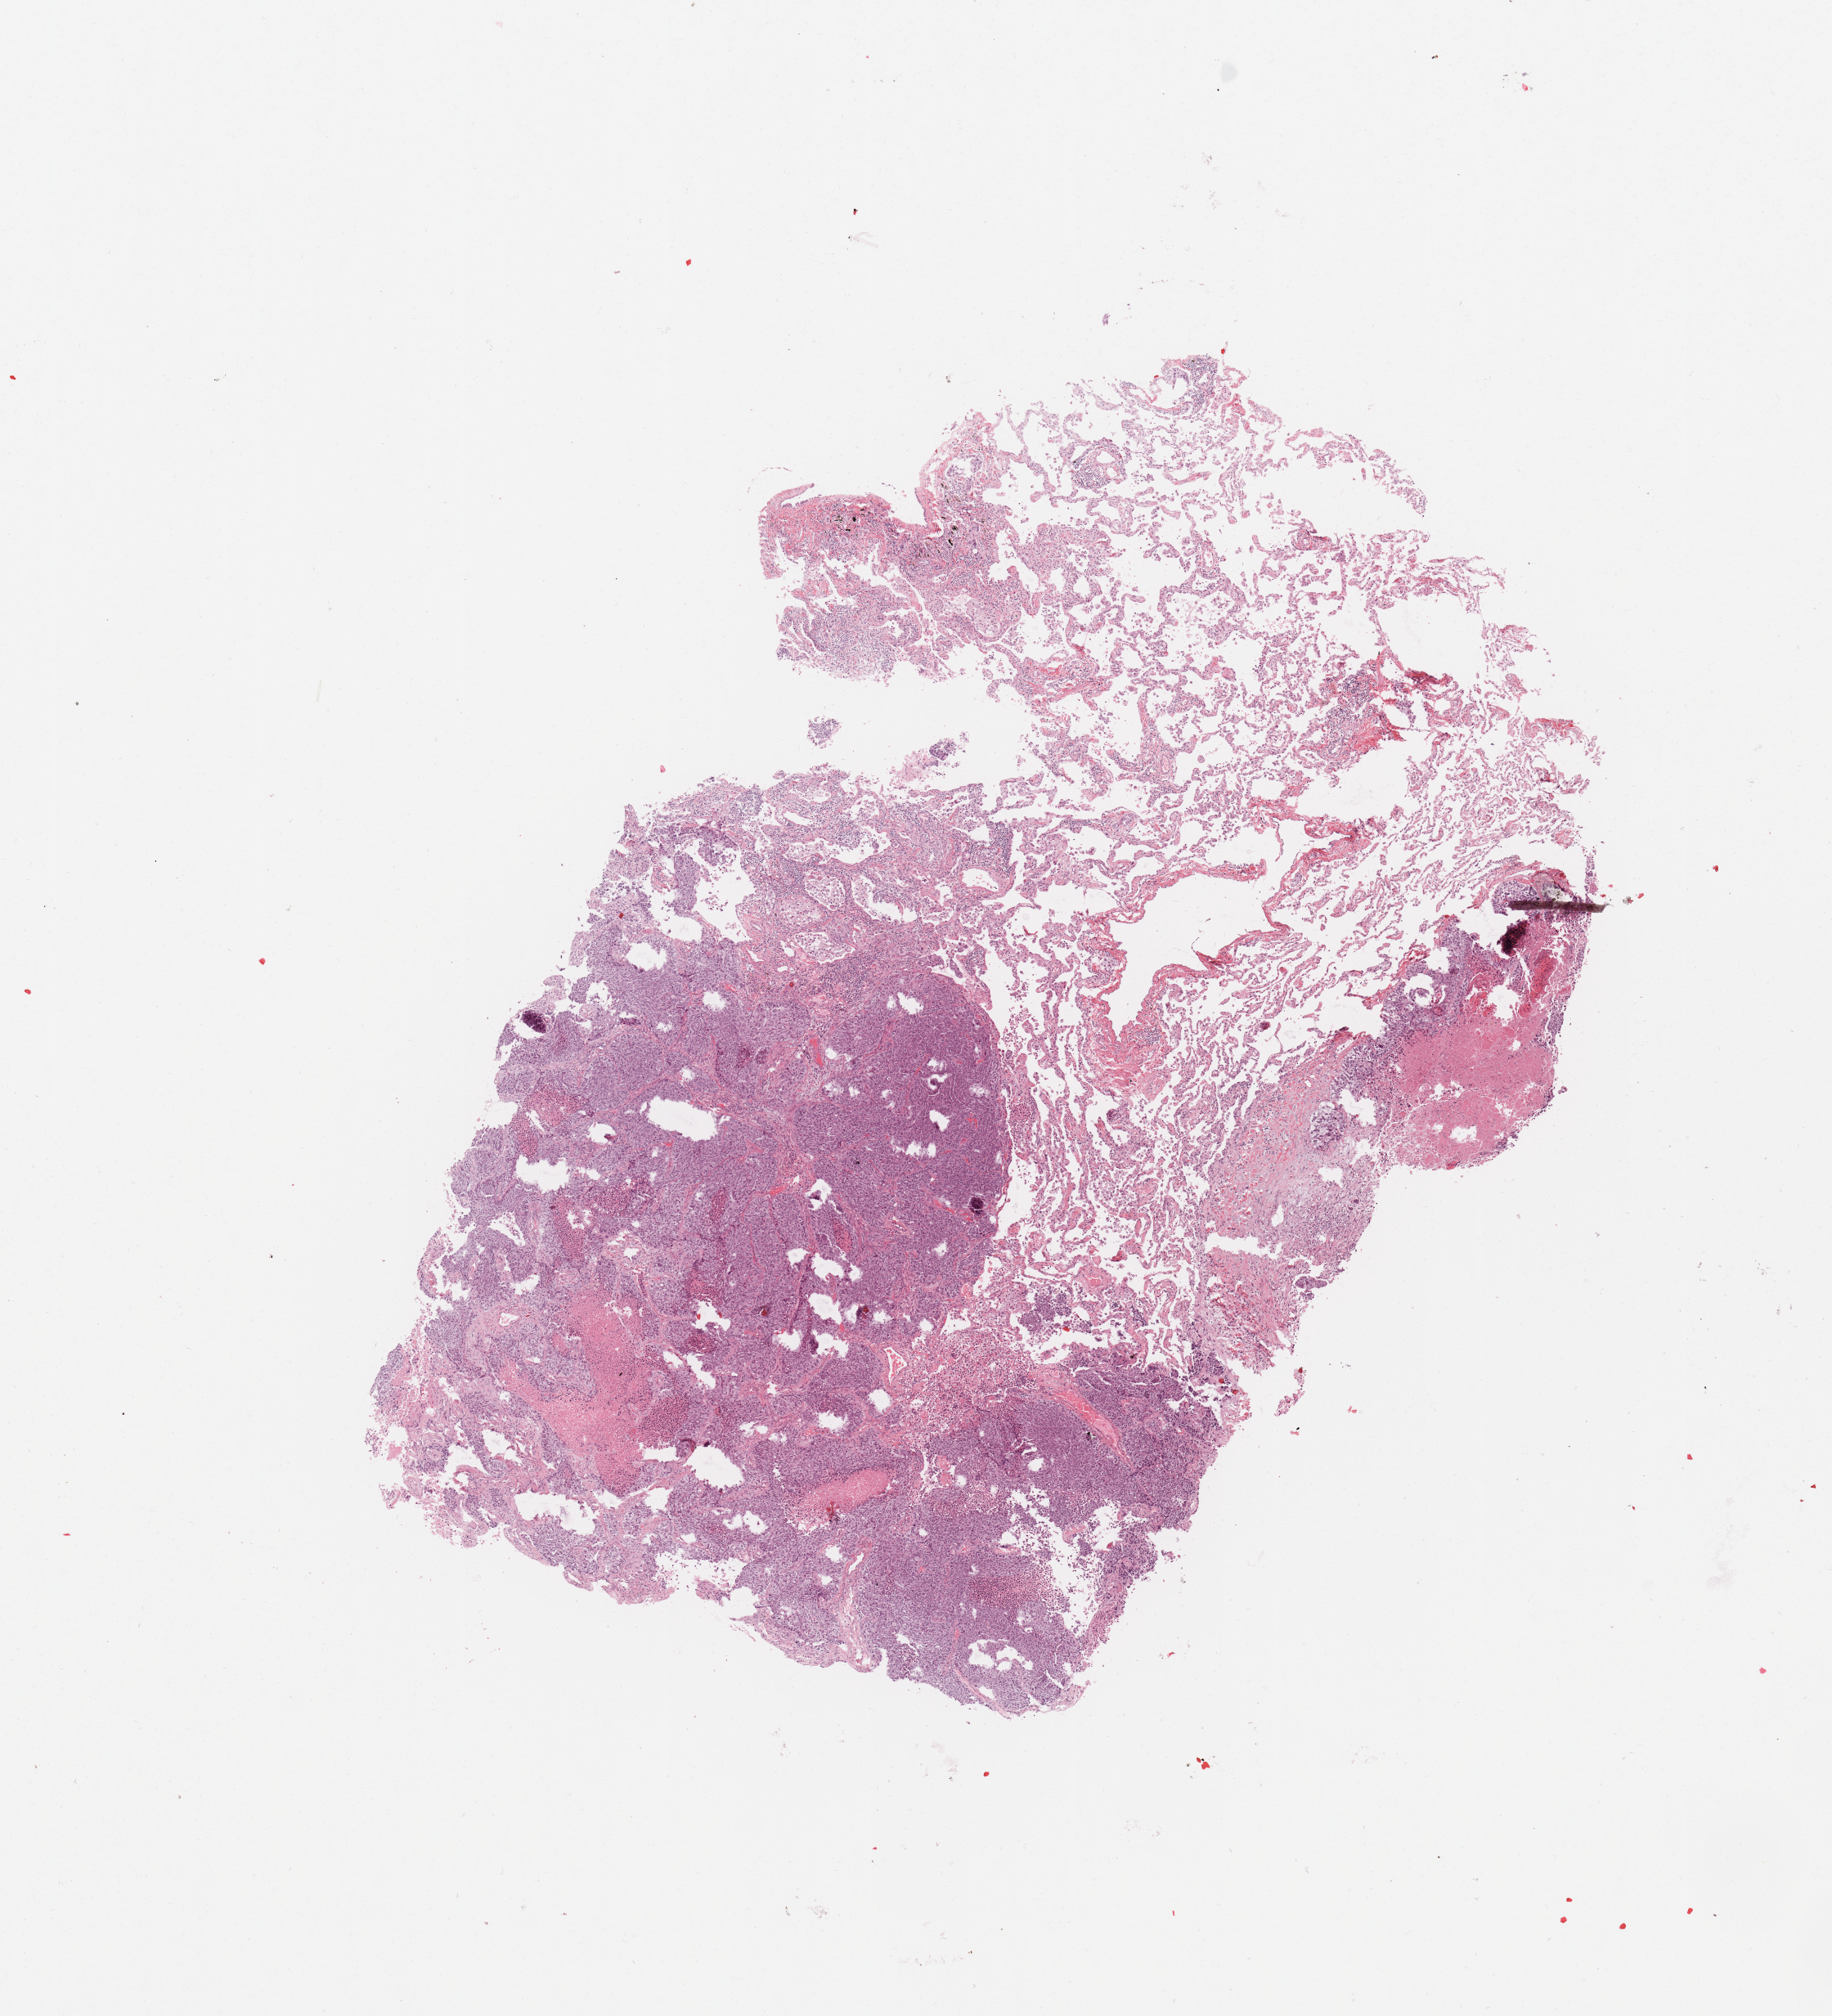
Whole-slide histology image, H&E — low-resolution overview of the scanned area, about 8.9 x 9.7 mm; tumour tissue sample, sampled site: lung. Patient: male, age 53 years.
Diagnosis: Squamous cell carcinoma, NOS.